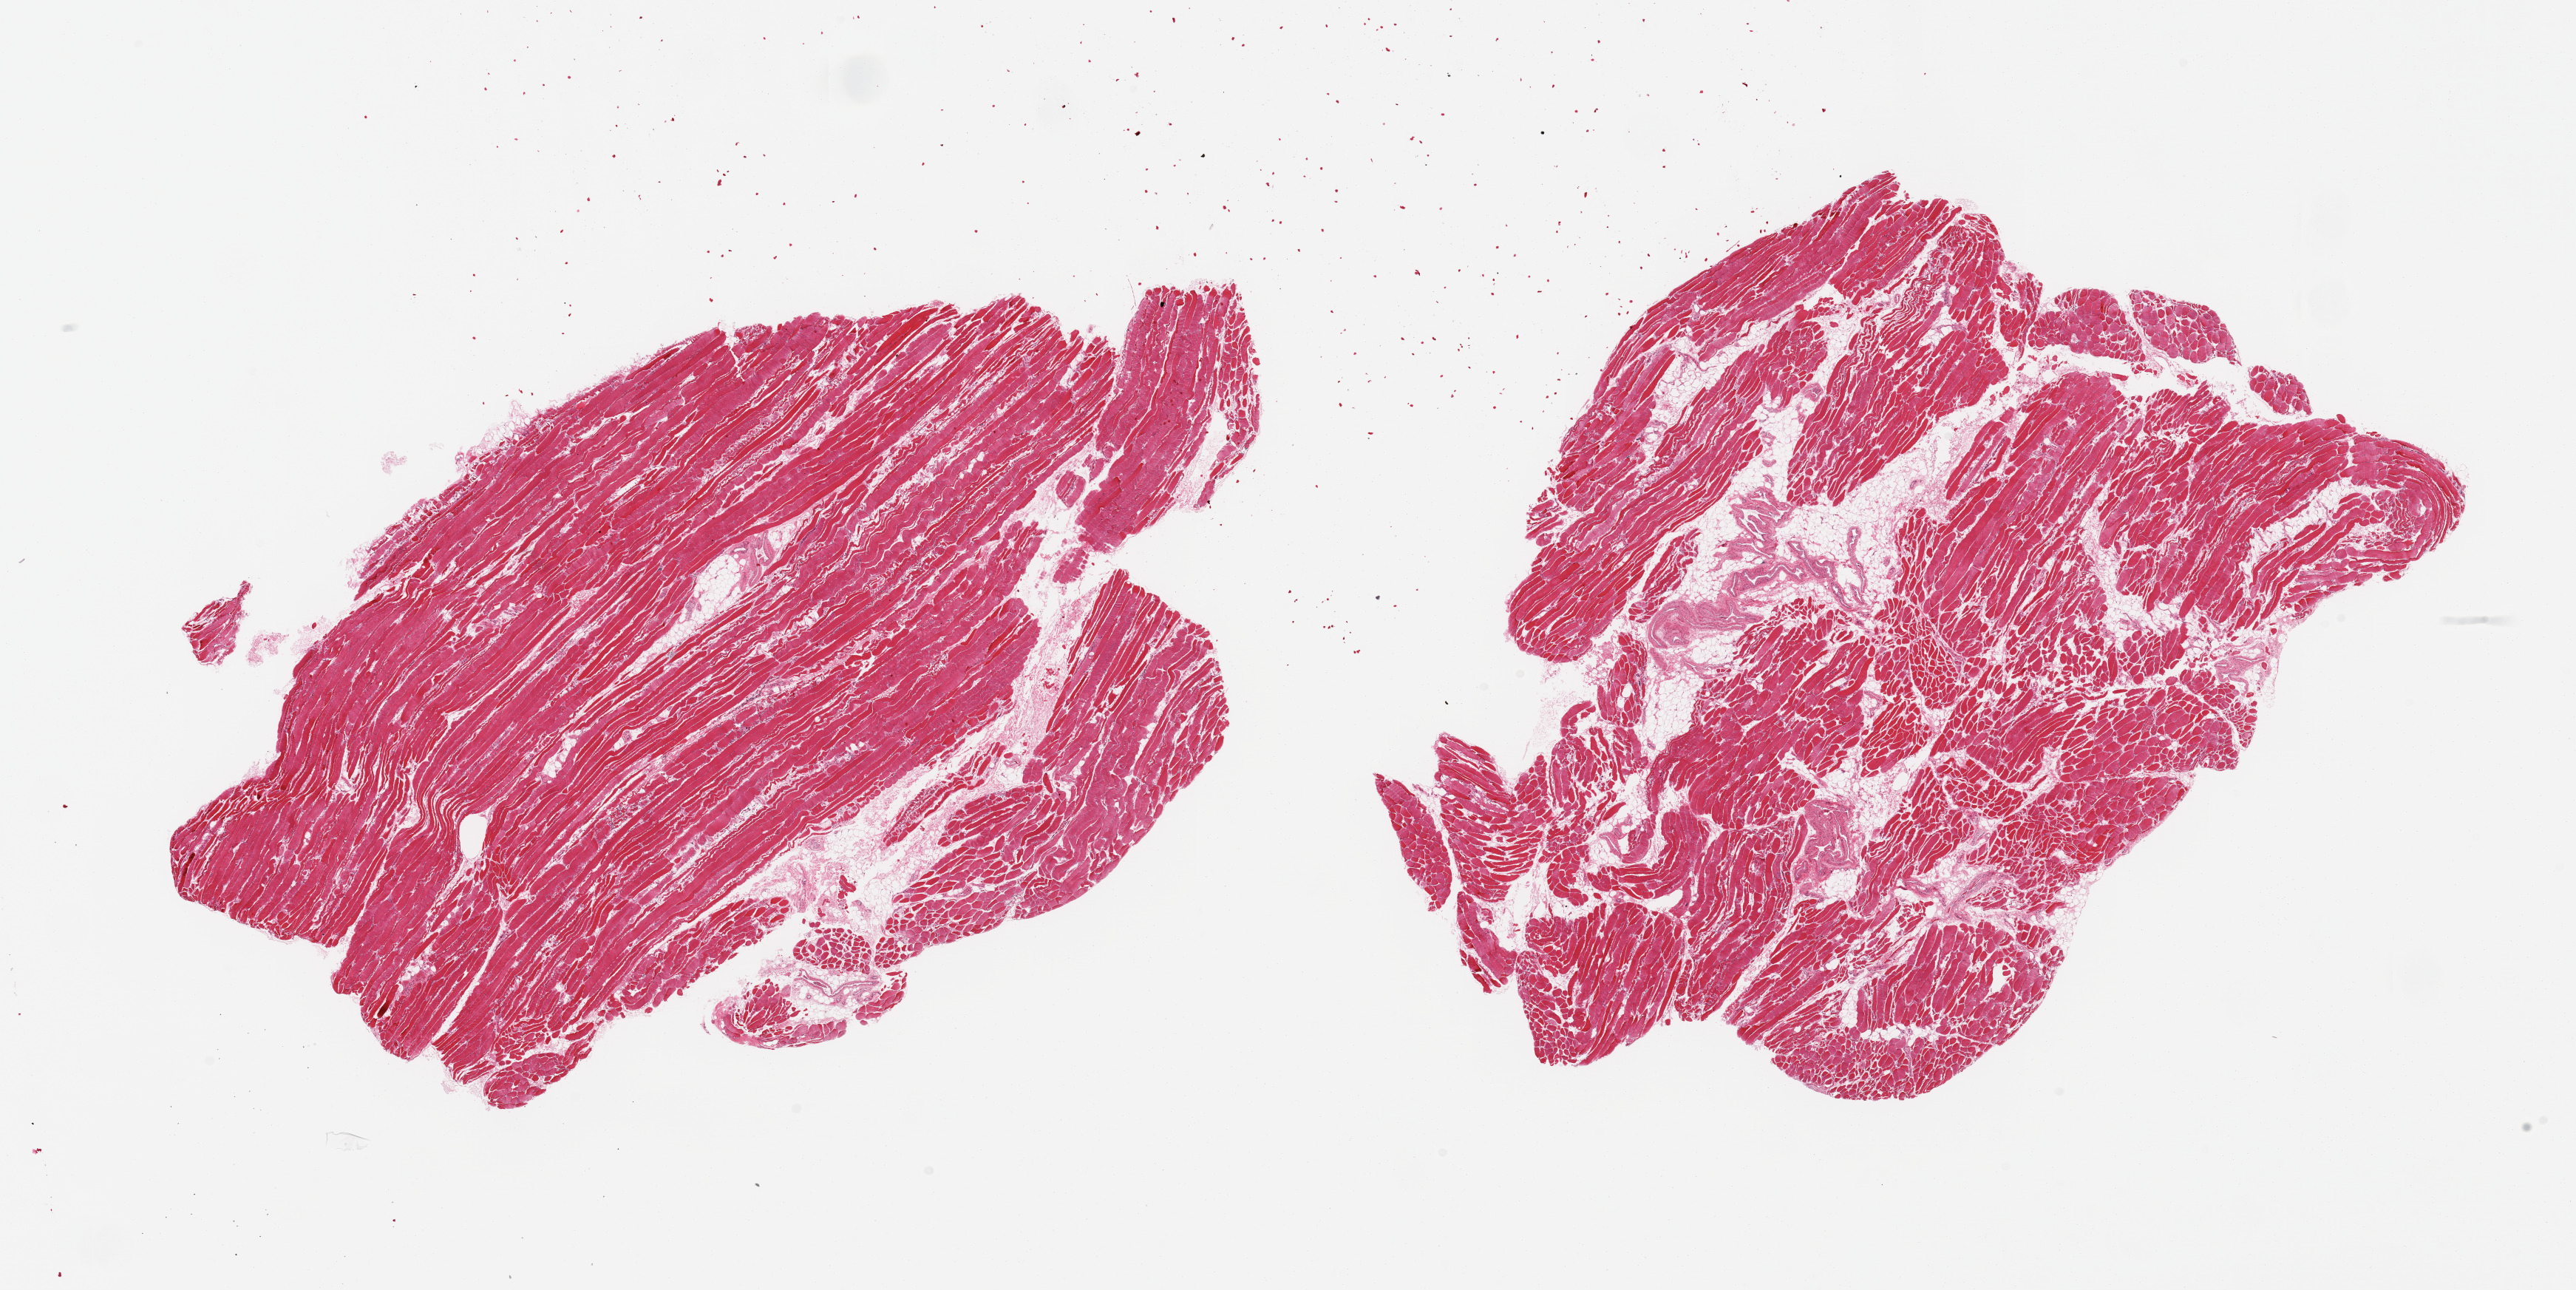
Hematoxylin and eosin (H&E) whole-slide image, brightfield — shown as a low-resolution overview of the whole scanned area (about 27.6 x 13.8 mm, acquisition: 20x scan), PAXgene-fixed, paraffin-embedded tissue, sampled site (target tissue): skeletal muscle, tissue donor sample. Donor: male.
Review note (as recorded): 2 pieces, interstitial fat/vascular elements are ~10-15% of tissue.